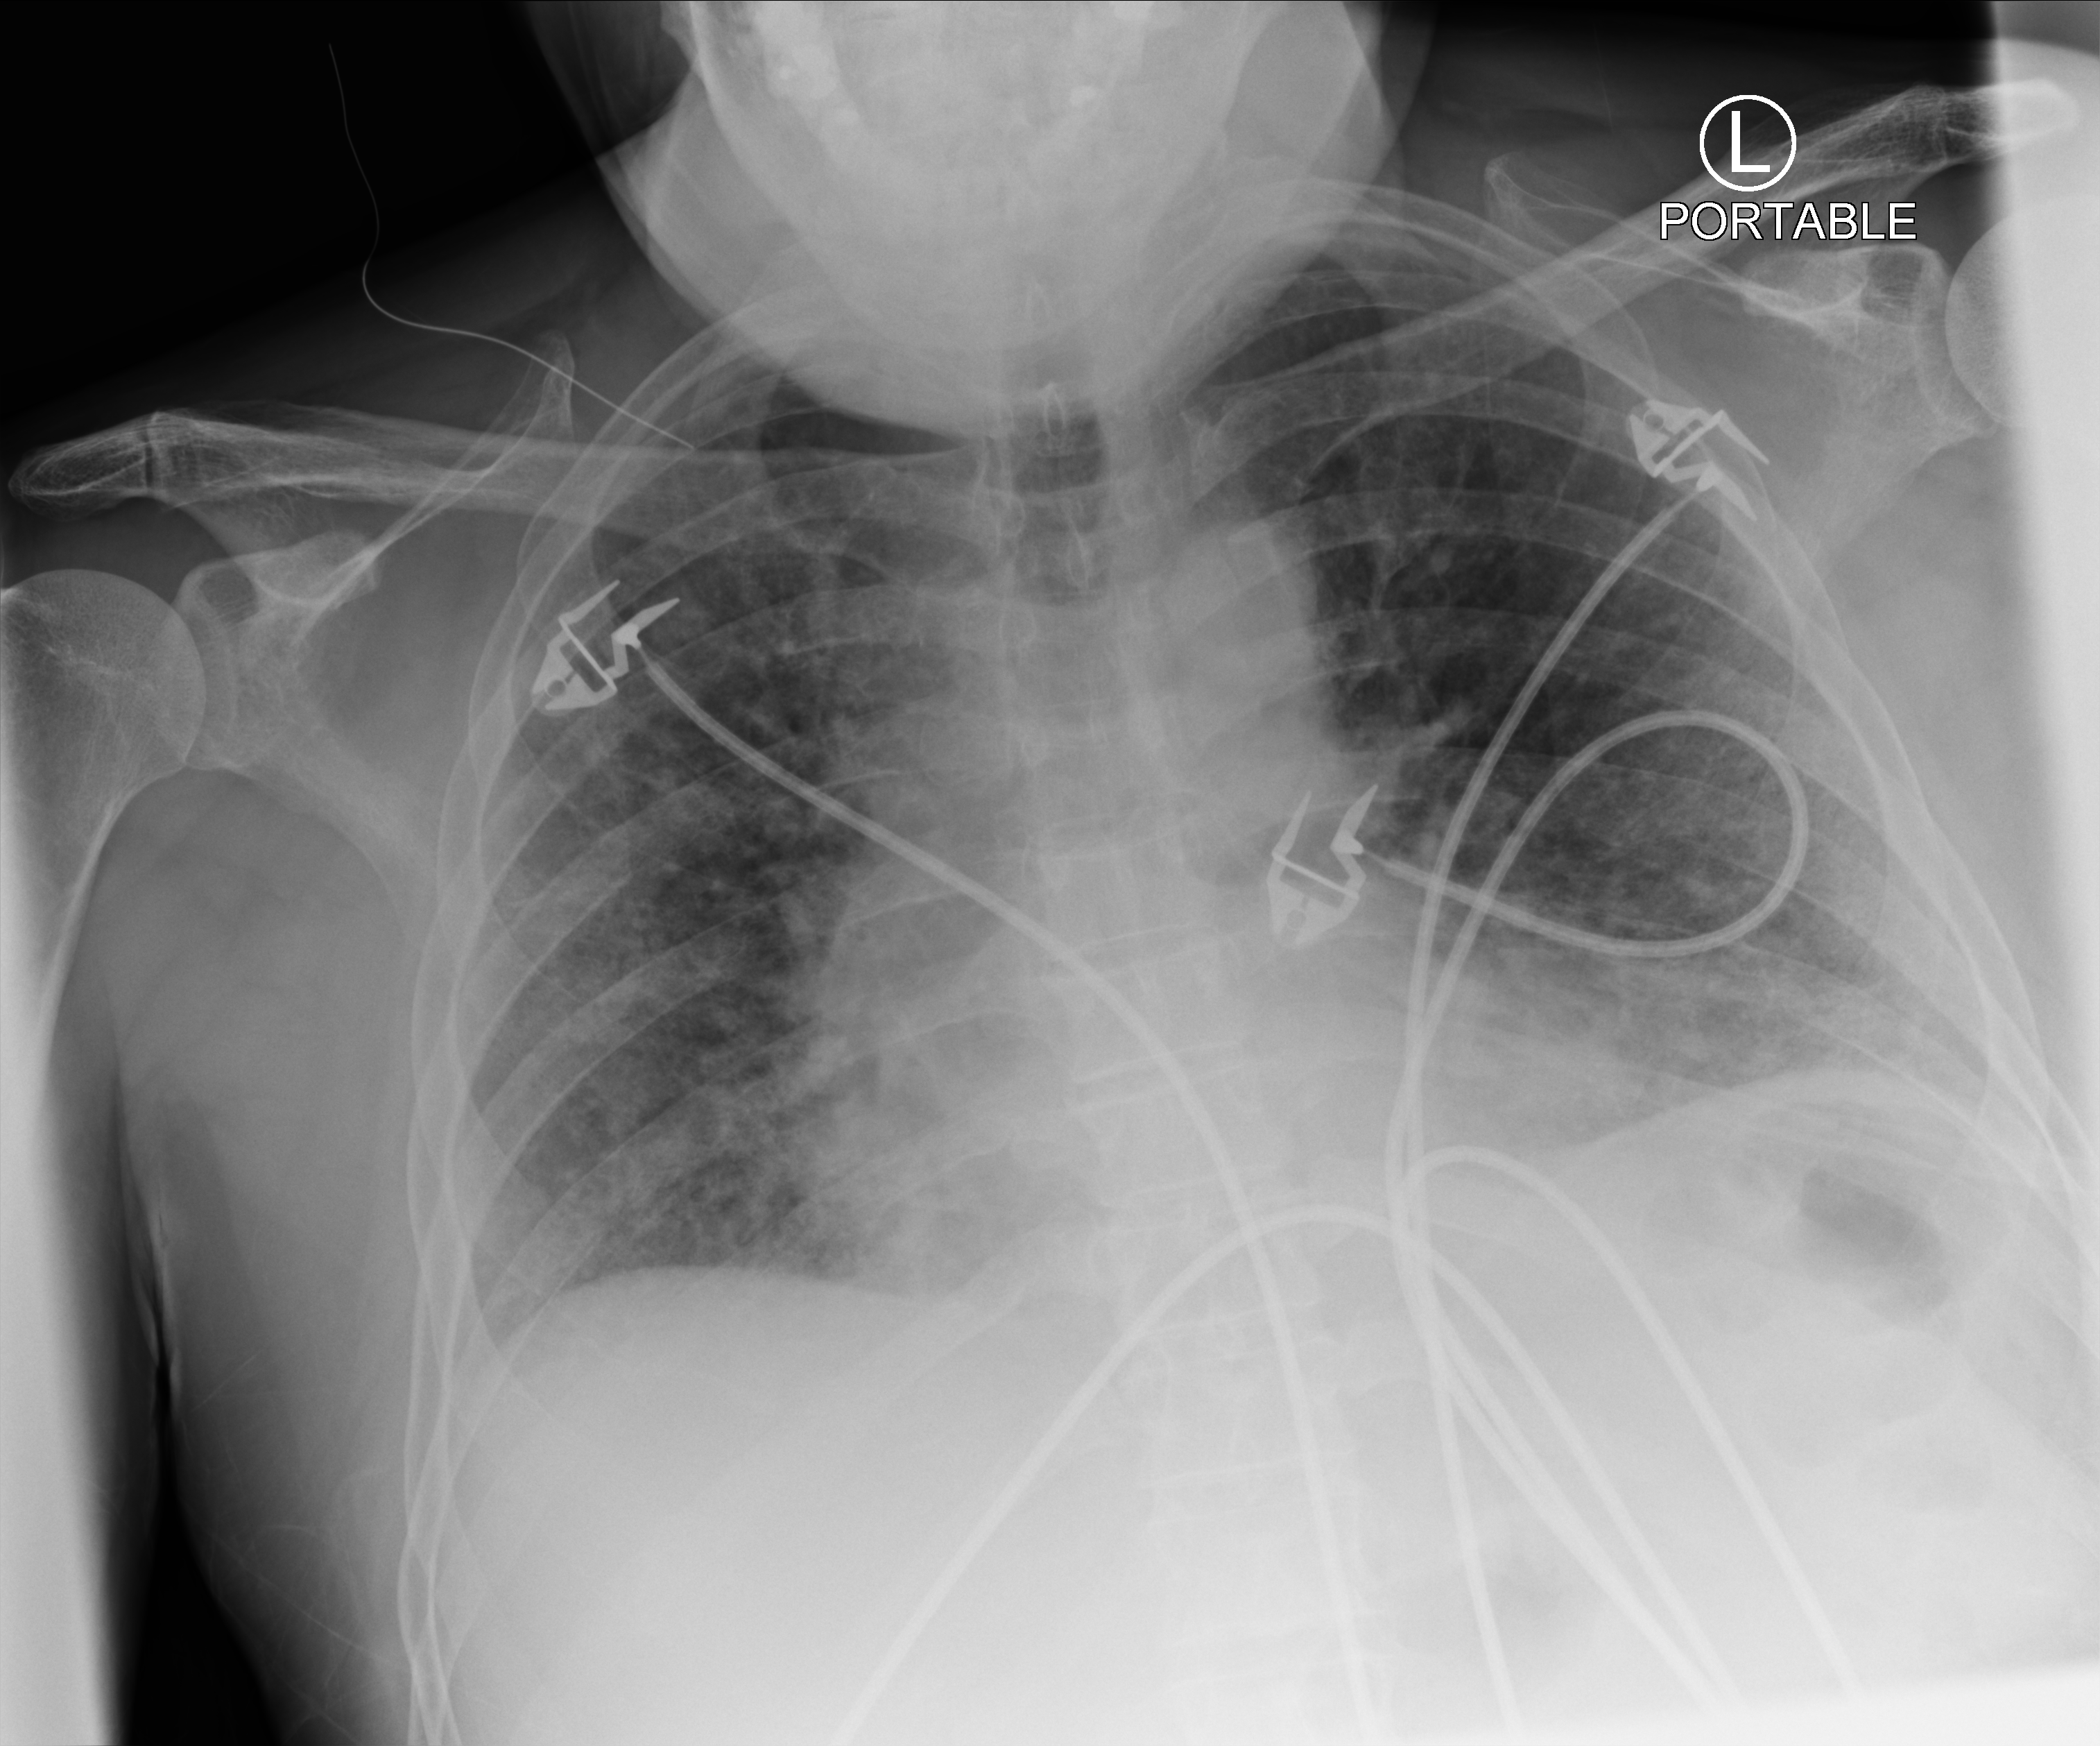
Chest X-ray (portable). Patient hospitalised with COVID-19; male, aged 60–74 years.
From the hospital-stay record, not from the radiograph (when in the stay this image was taken is not recorded):
- admitted to intensive care during this hospital stay: yes
- mechanically ventilated during this hospital stay: yes